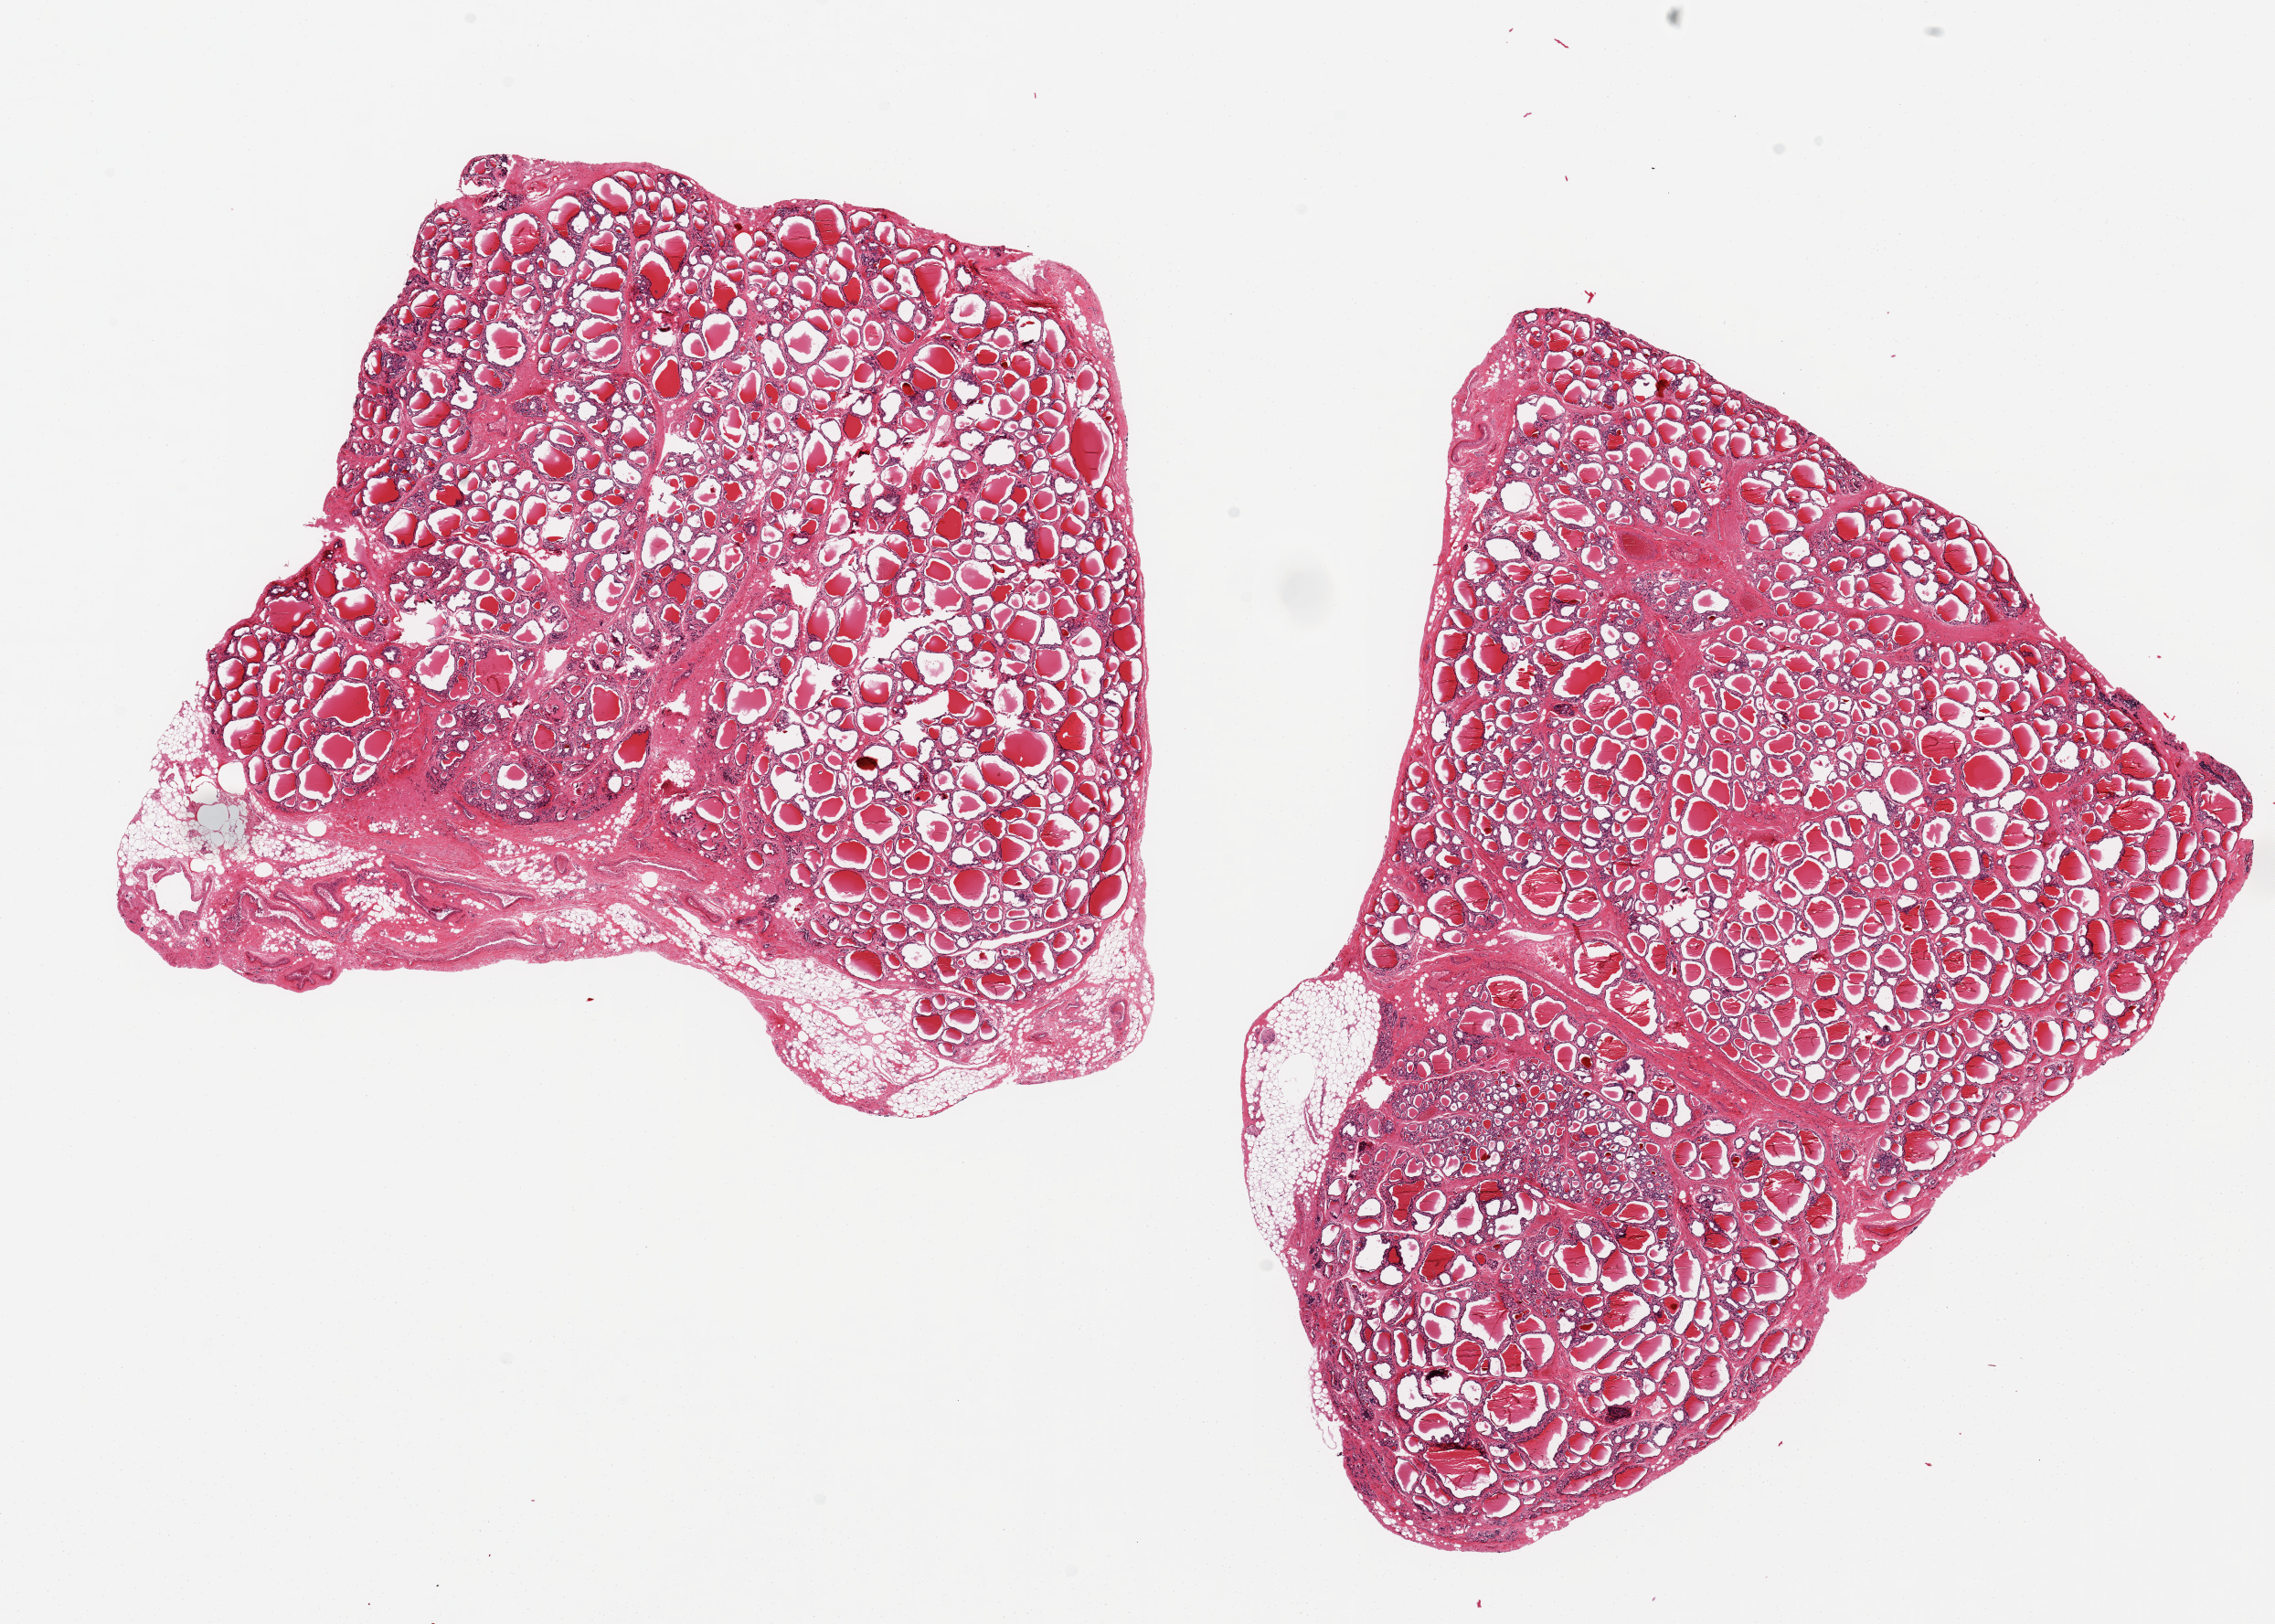
Digitized haematoxylin and eosin-stained section — low-resolution overview of the scanned area, about 19.7 x 14.1 mm (acquisition: 20x scan), PAXgene-fixed, paraffin-embedded tissue, target tissue: thyroid, donor tissue sample. Donor: female.
Review note (as recorded): 2 `7x8.5mm aliquots, relatively ???clean??? specimens.